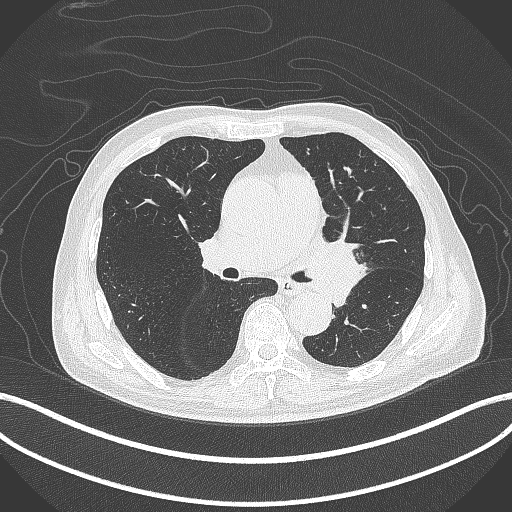
Chest CT, one axial slice; reconstruction kernel B70f; 120 kVp; lung window (W 1500 / L -600 HU); 1 mm slice thickness; 512 × 512 image matrix. Patient: male, 77 years. Case-level facts recorded for this patient, not image findings: clinical TNM (as recorded): T3 N1 M0.
Annotated regions visible in this slice (rectangle marked by the reading radiologist):
- lung tumour (recorded histology: adenocarcinoma): bounding box (x1, y1, x2, y2) in pixels: (305, 232, 370, 305)